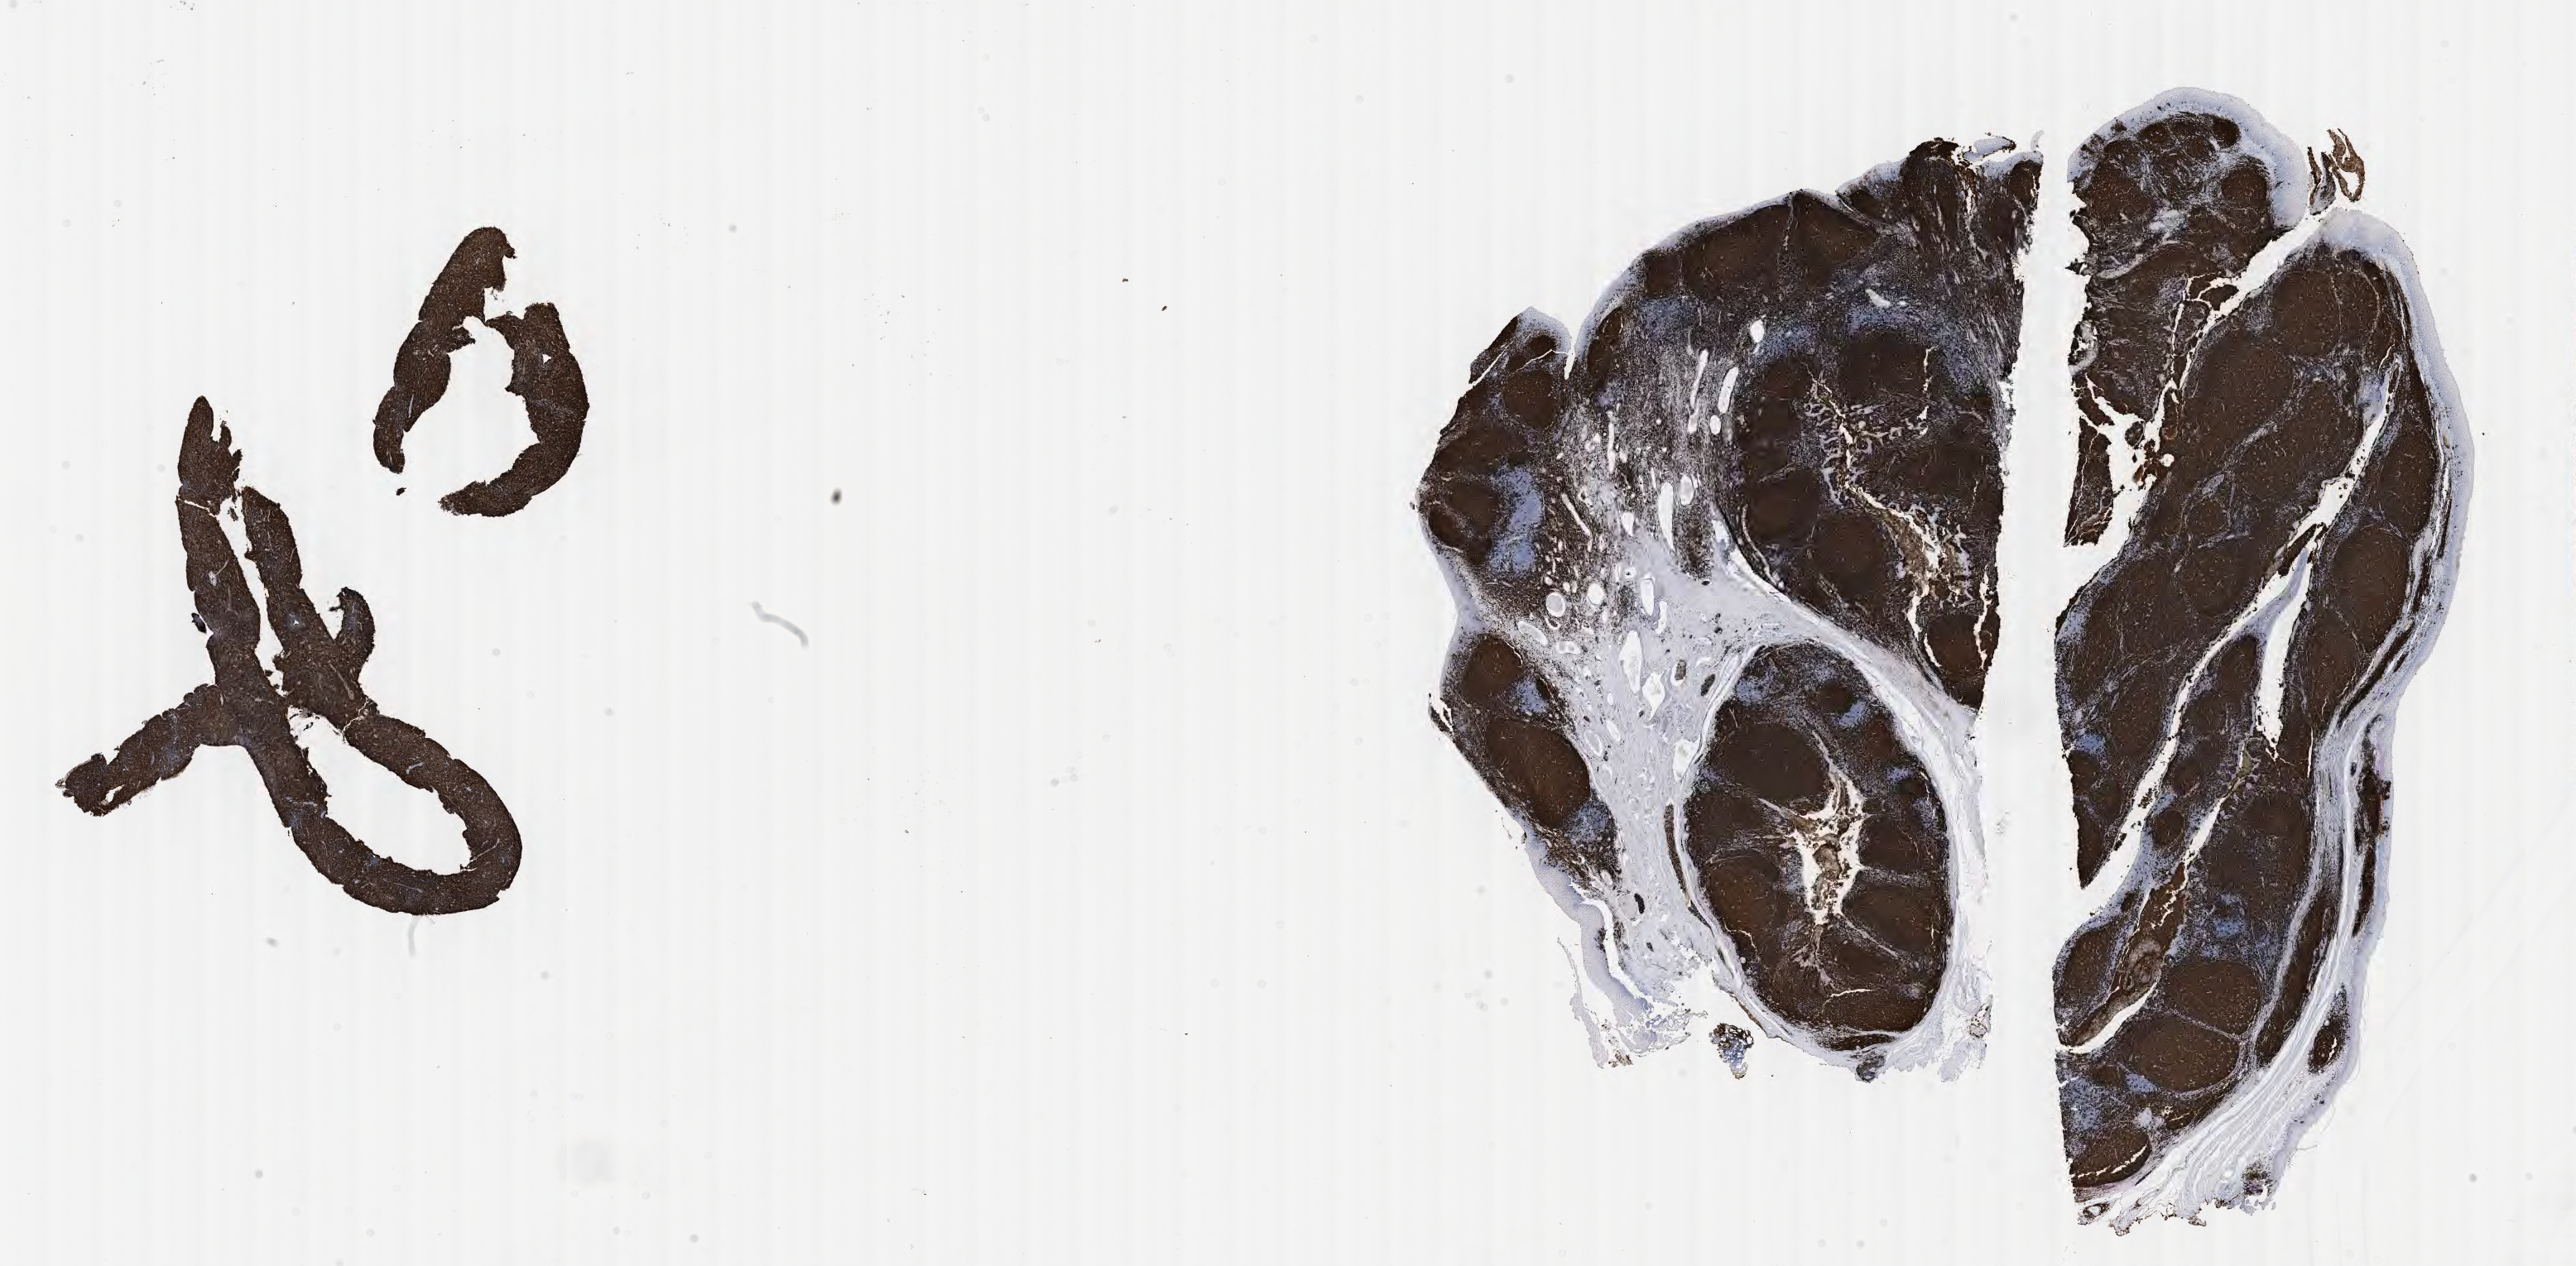
Whole-slide image, immunohistochemical stain for CD20, whole scanned area (about 25.1 x 12.4 mm) shown as a low-resolution overview. Male patient, 52 years old.
* specimen: tumor tissue; site: liver